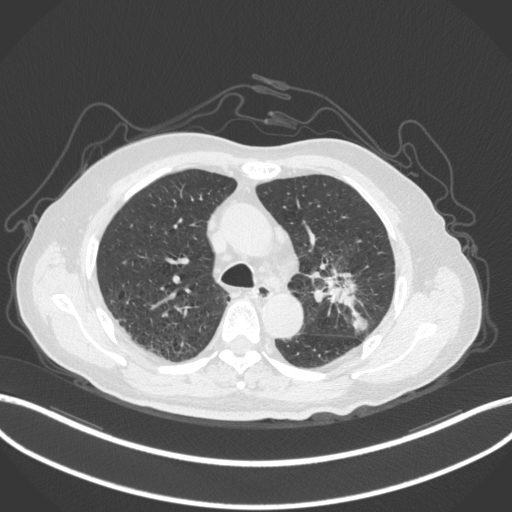
Chest CT, one axial slice. Position 193 of 331 along the scan axis. Reconstruction kernel B31f. 120 kVp. Lung window (W 1500 / L -600 HU). 1 mm slice thickness. 512 × 512 image matrix, field of view 400 × 400 mm. Patient: male, 79 years. From the clinical record (not read from this slice): clinical TNM (as recorded): T2a N1 M1; histopathological grade: G3.
Structures marked on this image (bounding box drawn by a radiologist):
- lung tumour (recorded histology: adenocarcinoma): bounding box <323,269,373,337> (left, top, right, bottom; pixels)